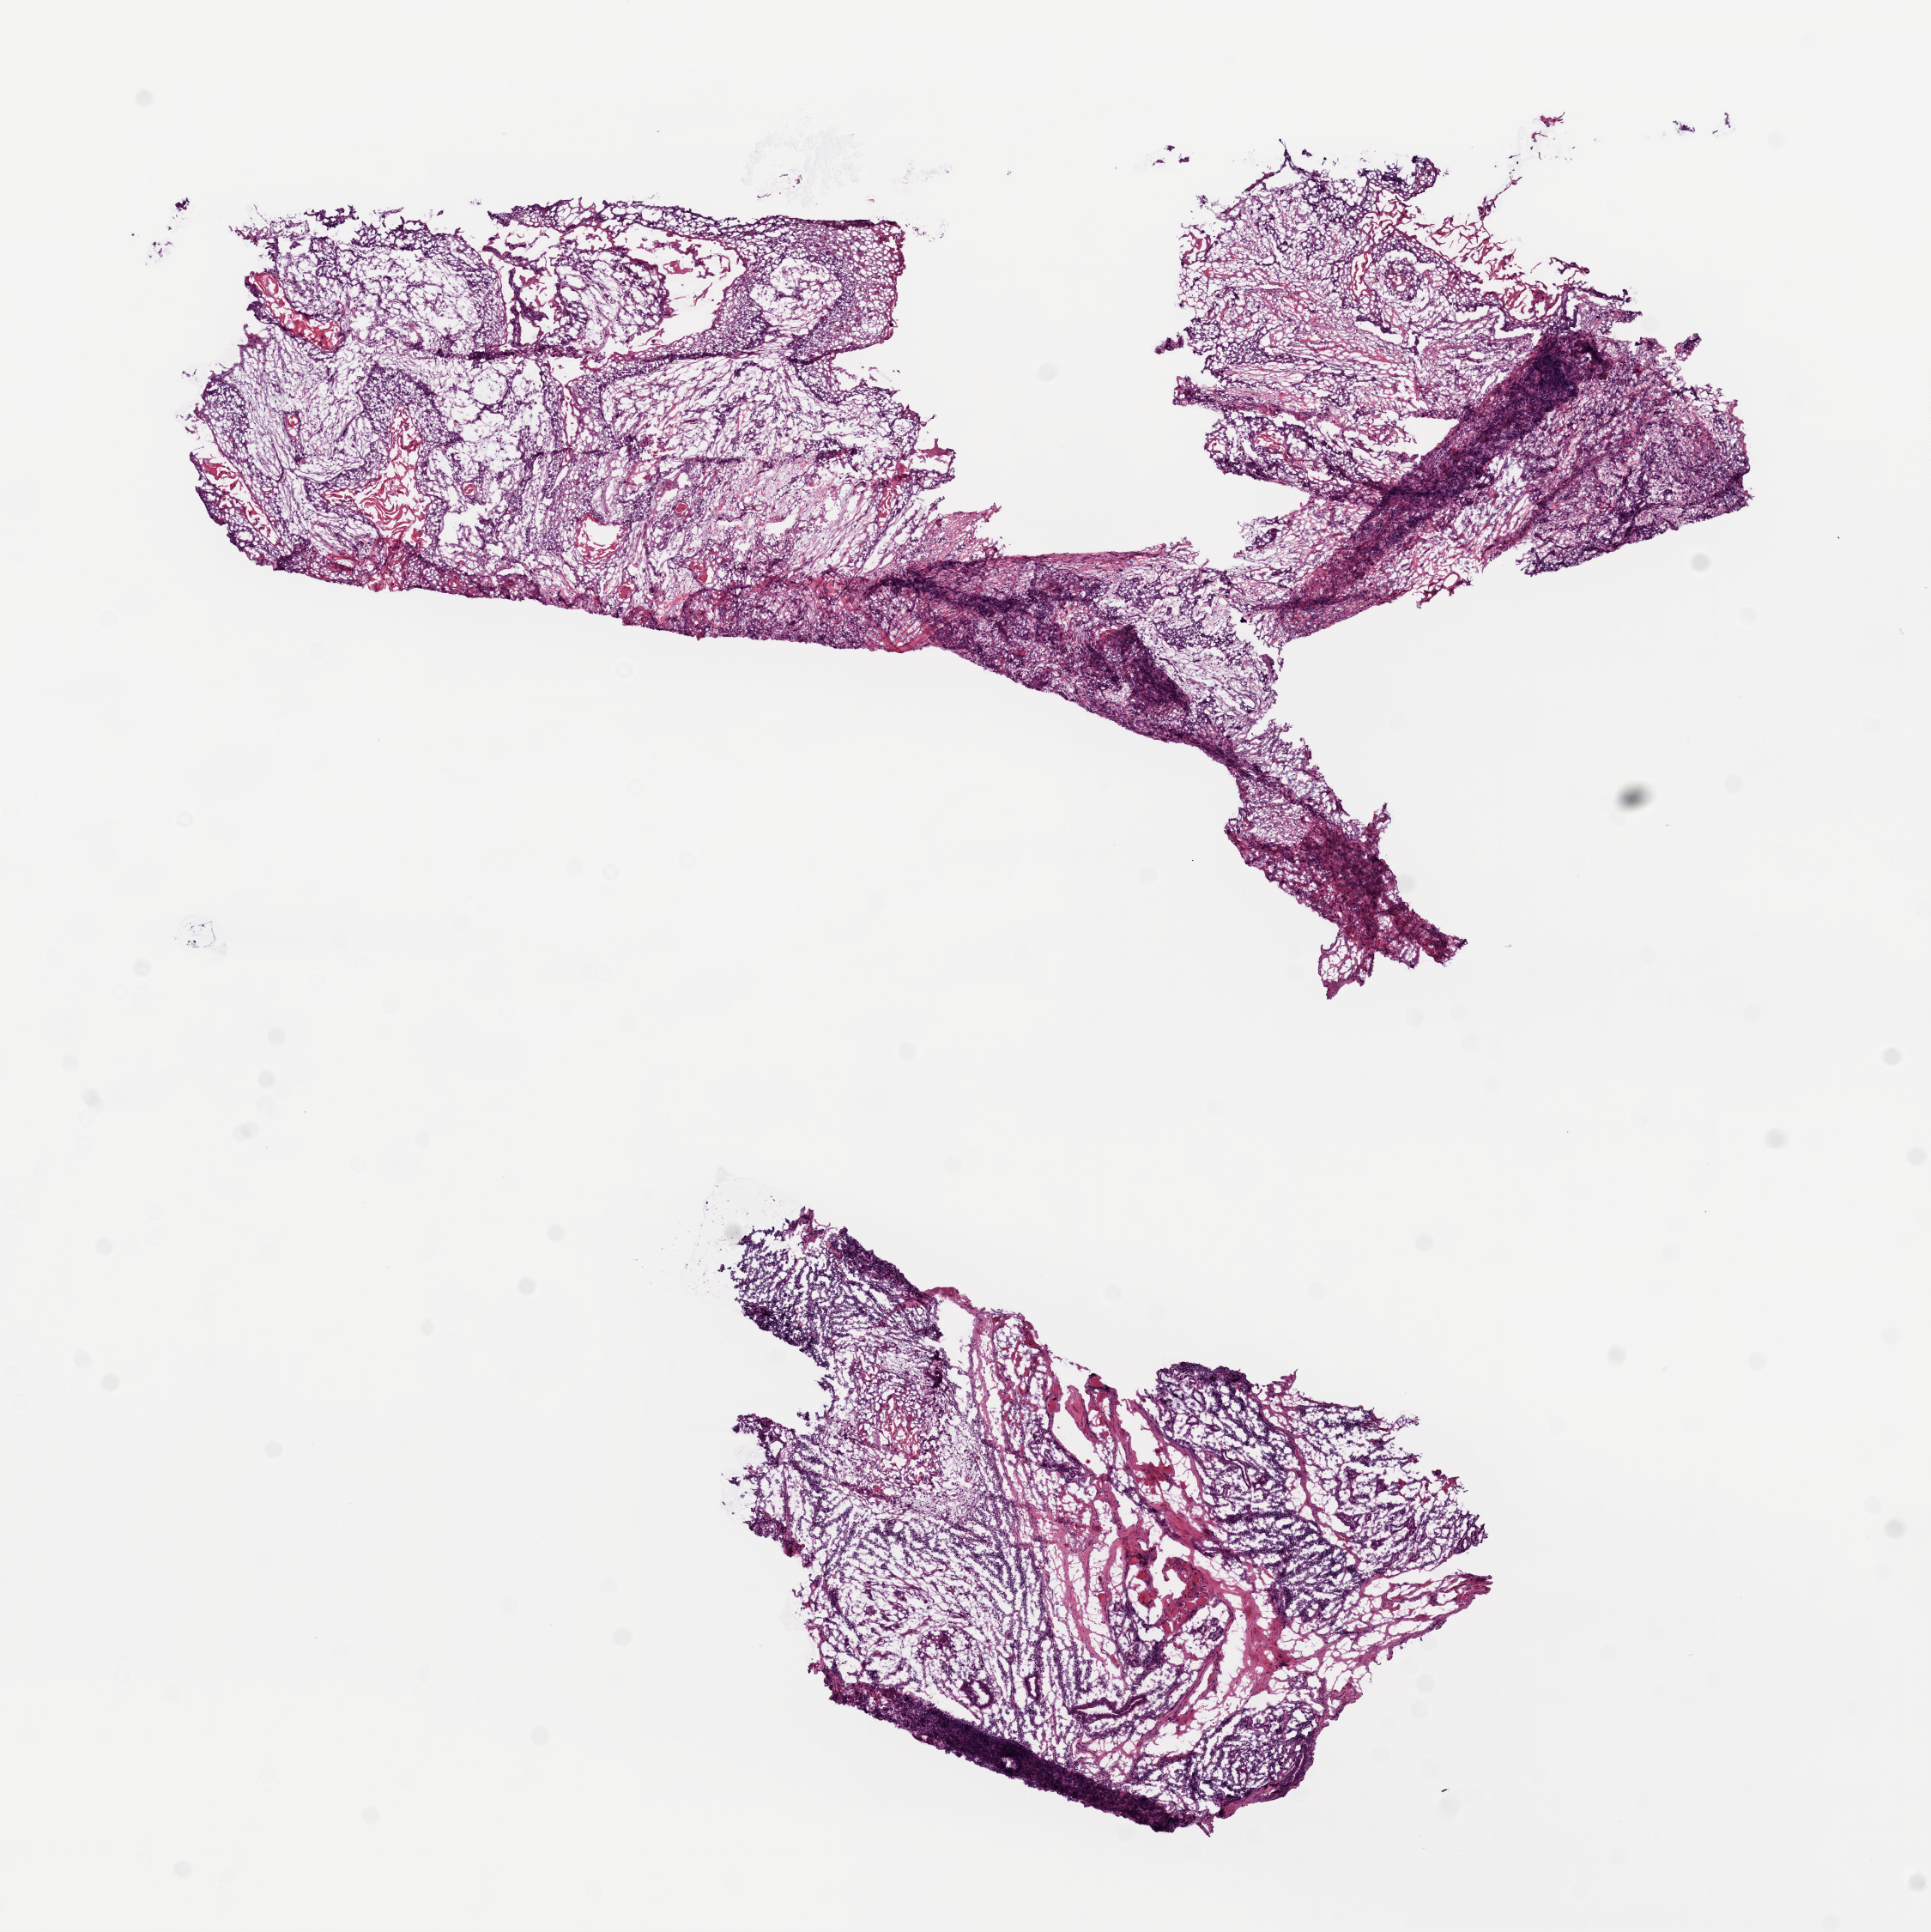
Whole-slide histology image, Hematoxylin and eosin (H&E) stained — a low-resolution overview of the entire scanned area, about 9.0 x 9.0 mm. Frozen section from the bottom of the tissue portion. Sample: primary tumour, head and neck. Male, age 68 years at initial diagnosis. Histologic grade: G3 (poorly differentiated). Composition of this section per pathologist review: tumour cells 50%, tumour nuclei 60%, normal cells 0%, stromal cells 50%, necrosis 0%.
• TNM: T3 N0
• lymph nodes positive (case pathology): 0 of 65 examined
• pathologic diagnosis: Squamous cell carcinoma, NOS (larynx, NOS)
• AJCC pathologic stage: III (7th edition)